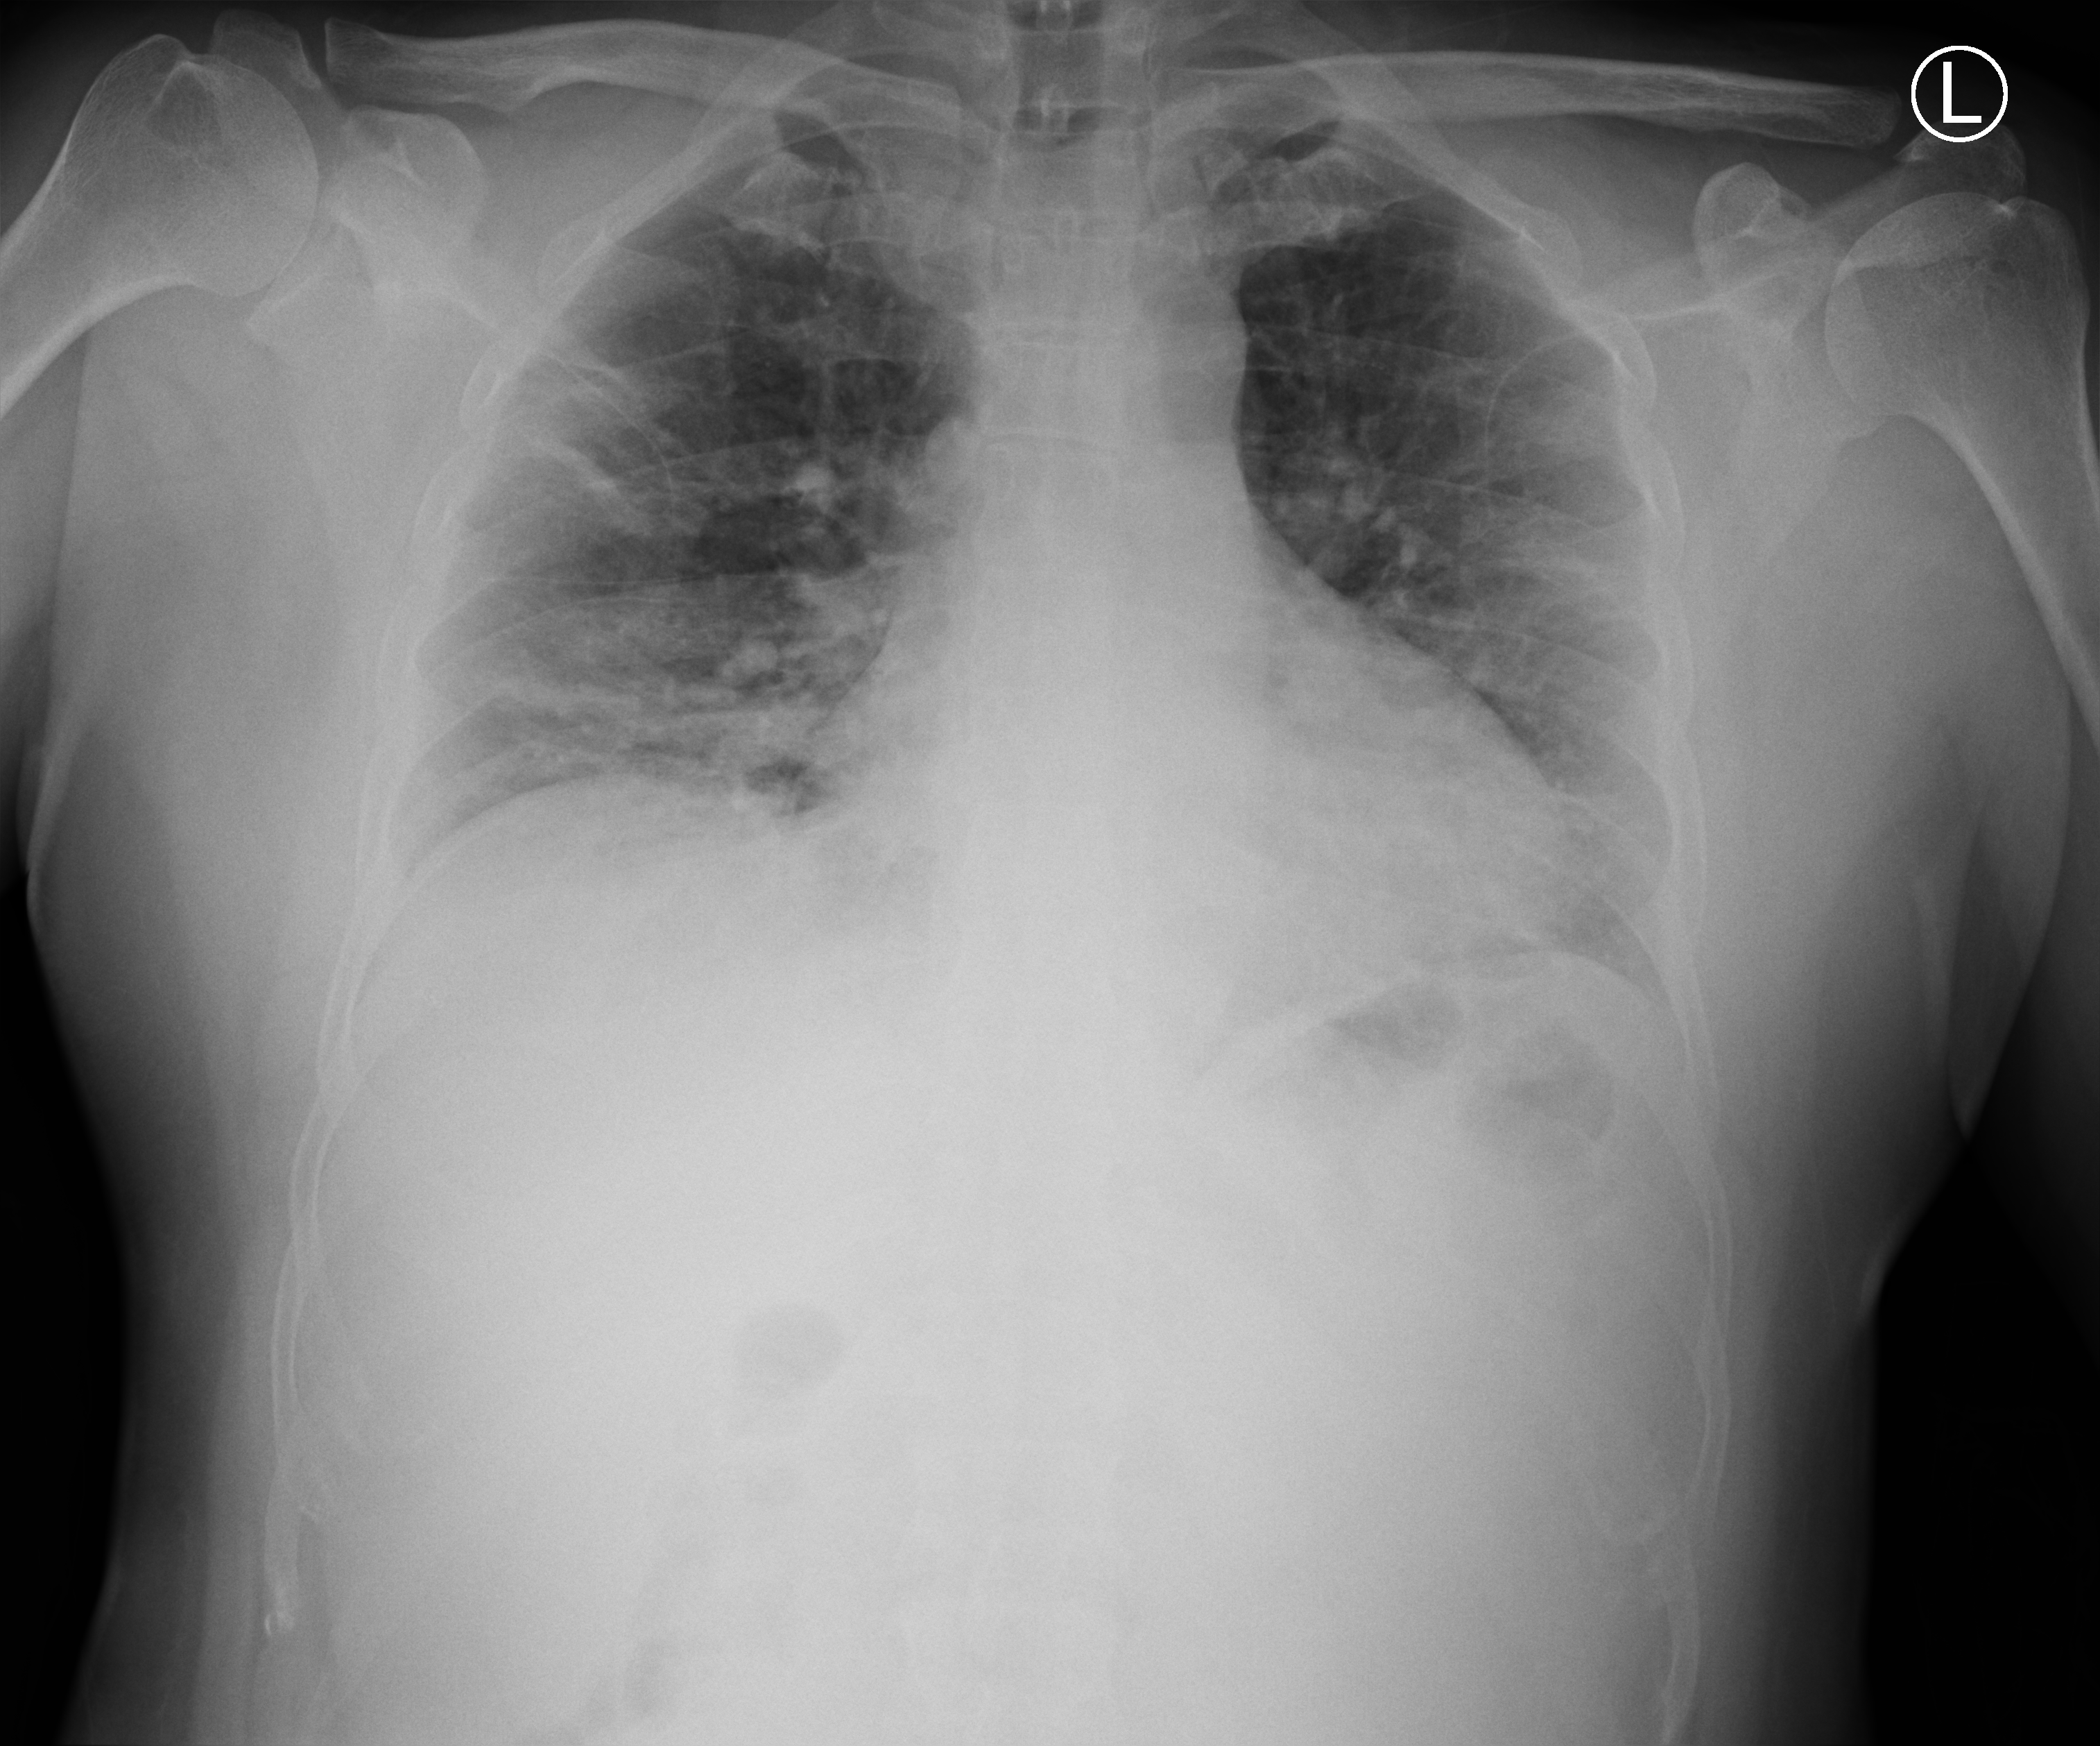
Portable chest radiograph; anteroposterior (AP) projection. Patient hospitalised with COVID-19; male, aged 18–59 years.
Hospital-stay facts (about this admission, not read from this image; timing relative to this image not recorded): diabetes (admission record): no; length of hospital stay: 7 days.